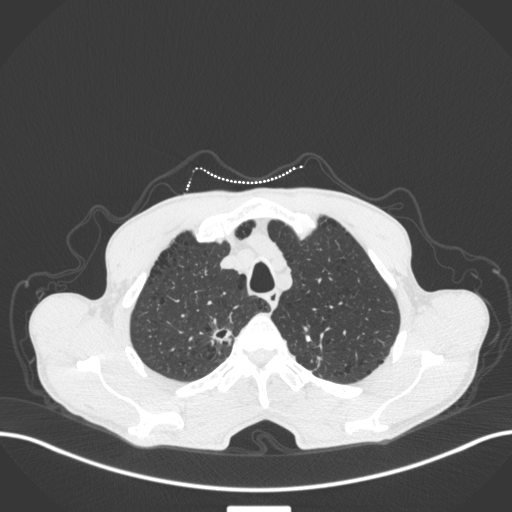
Chest CT, one axial slice. Position 359 of 445 along the scan axis. Reconstruction kernel B31f. 120 kVp. Lung window (W 1500 / L -600 HU). 1 mm slice thickness. 512 × 512 image matrix. Patient: male, 70 years. From the clinical record (not read from this slice): clinical TNM (as recorded): T1a N0 M0.
Annotated regions visible in this slice (bounding box drawn by a radiologist):
- lung tumour (recorded histology: adenocarcinoma): box from (x=207, y=317) to (x=237, y=350) px